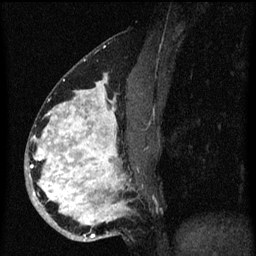
Breast MRI (dynamic contrast-enhanced), one sagittal slice; position 30 of 60 along the scan axis; dynamic contrast-enhanced series, image 2 of 3 at this slice position (ordered by acquisition); 1.5 T; TE 4.2 ms, TR 8.4 ms; 256 × 256 image matrix, field of view 180 × 180 mm. Female patient, age 34 years. From the clinical record (not read from this slice): setting: breast cancer imaged before/during neoadjuvant chemotherapy; receptor status: HR-positive, HER2-negative.
Structures marked on this image (semi-automatically segmented with operator editing):
- analysis volume of interest (the breast-tissue region the enhancement analysis was run in; not a lesion): bounding box (x1, y1, x2, y2) in pixels: (26, 58, 155, 243)
- tumour enhancement mask (voxels above the 70 % enhancement threshold inside the analysis volume of interest): (30, 78, 131, 239)